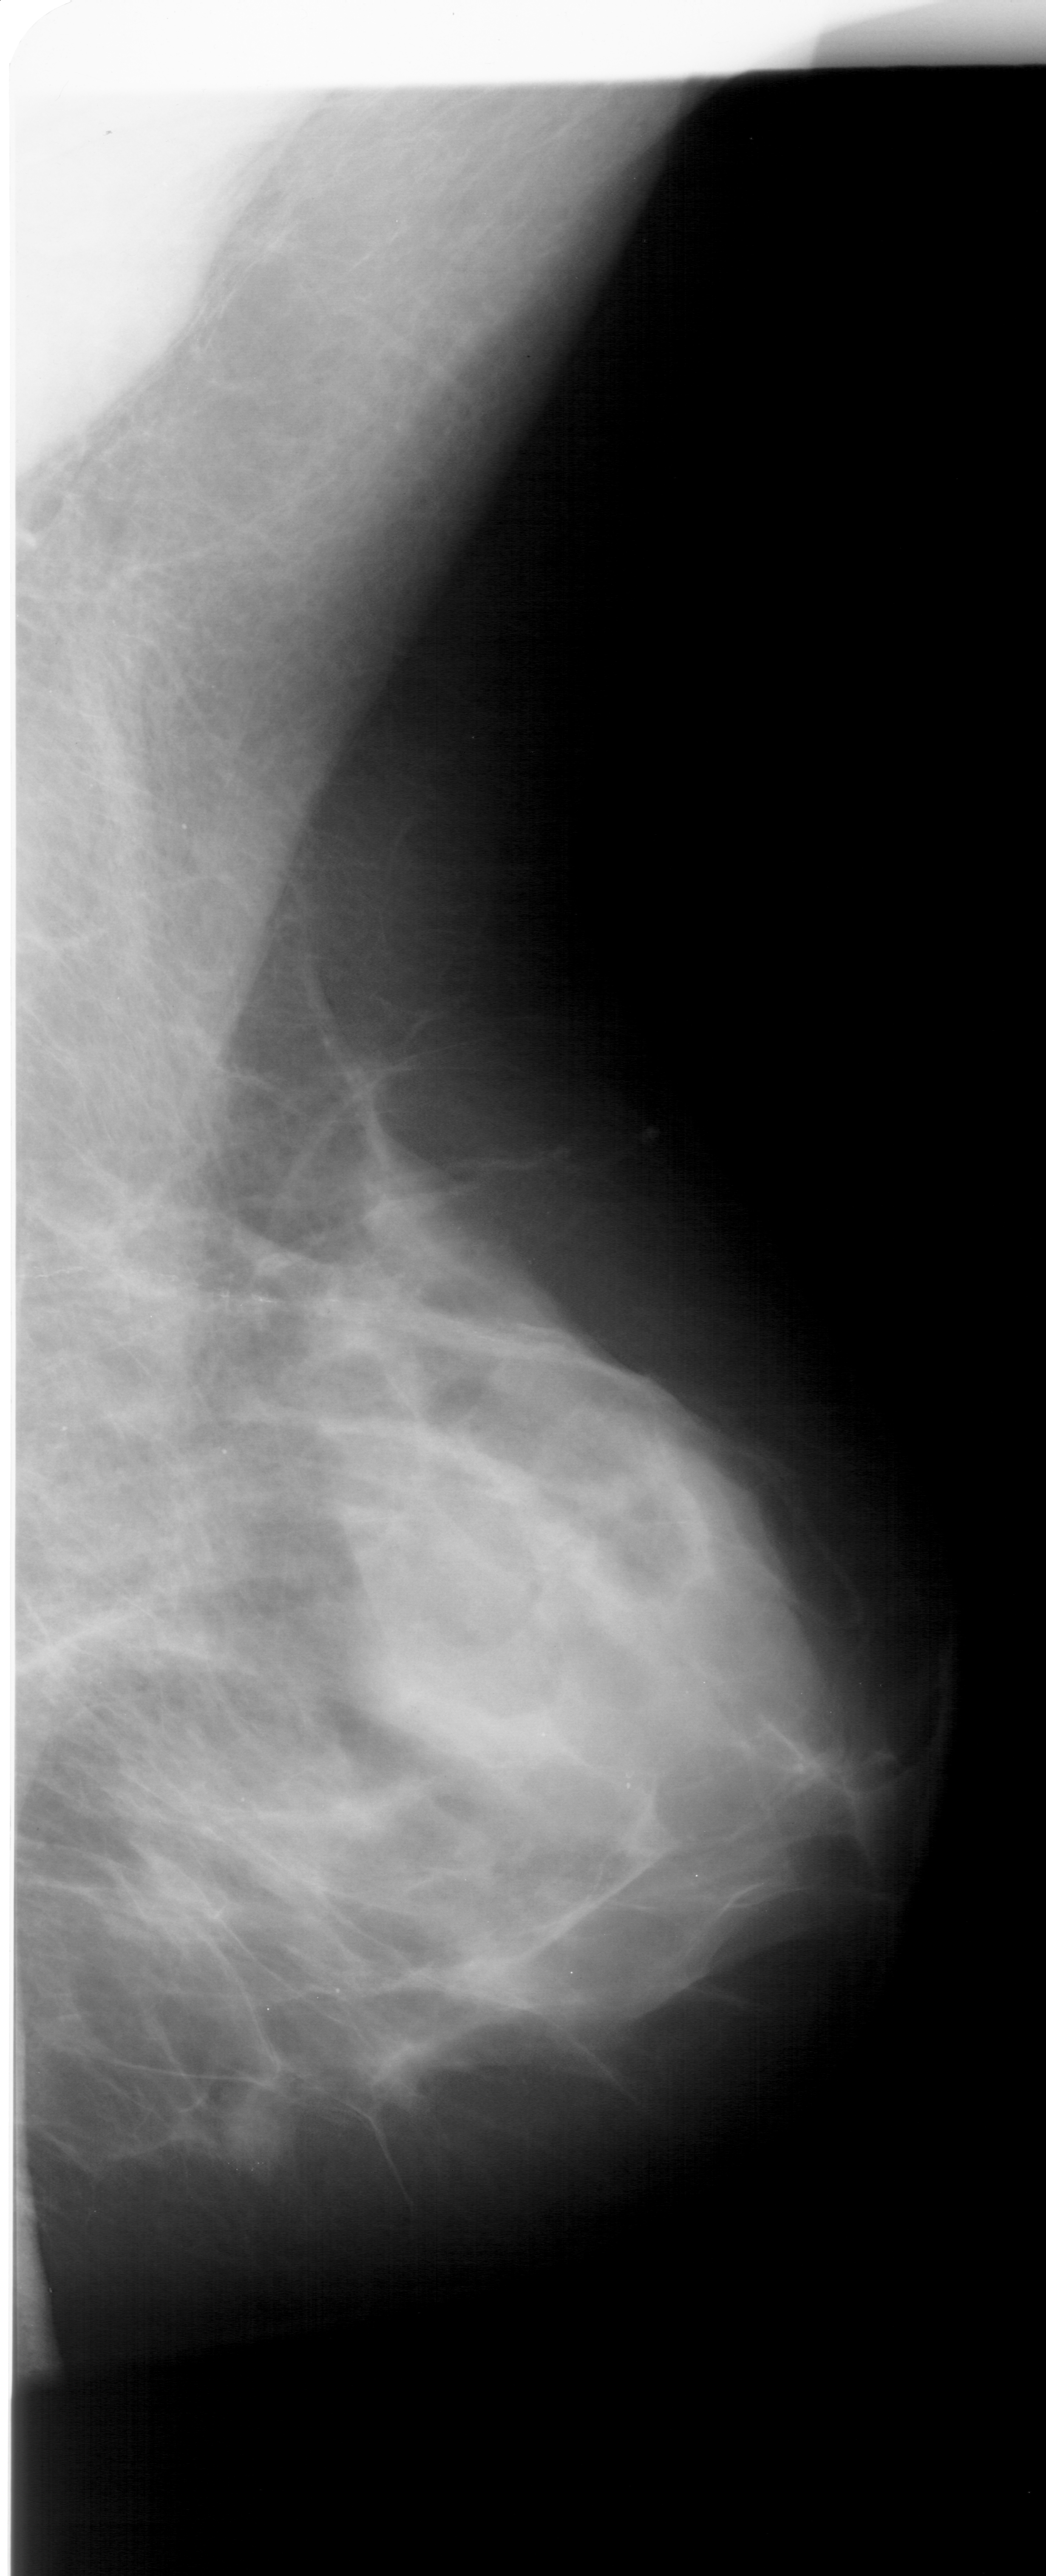
Mammogram (digitized film). Right breast. MLO view. 1046 × 2576 image matrix.
Expert-marked regions of interest on this image (one box per marked abnormality):
- mass, shape lobulated, margins circumscribed; BI-RADS assessment category 4; subtlety rating 3 on a 1 (subtle) to 5 (obvious) scale; pathology (as recorded): benign: bounding box (x1, y1, x2, y2) in pixels: (221, 2099, 292, 2177)